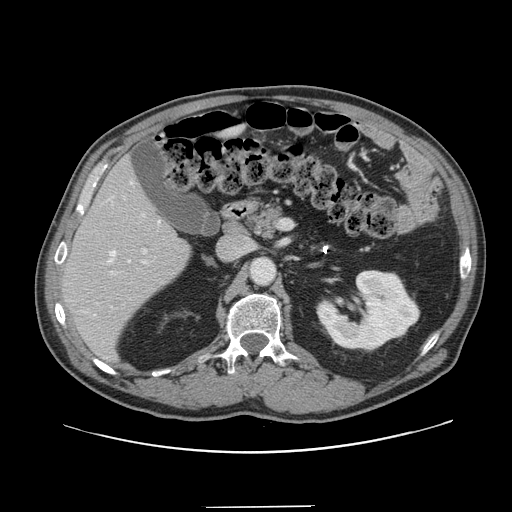
Contrast-enhanced abdominal CT, one axial slice; slice 77 of 139 in the series (ordered by position); intravenous contrast given; soft-tissue window (W 400 / L 40 HU); 2.5 mm slice thickness; 512 × 512 image matrix, field of view 397 × 397 mm. Male patient, age 64 years. Case-level facts recorded for this patient, not image findings: diagnosis: colorectal cancer liver metastases, imaged before liver resection; multiple liver metastases: yes; largest metastasis: 3.5 cm; disease in both lobes: yes.
Annotated regions visible in this slice (manually delineated by an expert):
- hepatic veins: bounding box <94,182,161,316> (left, top, right, bottom; pixels)
- liver: <63,161,190,360>
- planned liver remnant (the part of the liver to remain after resection): <63,161,190,359>
- portal vein (with intrahepatic branches): <110,249,147,274>